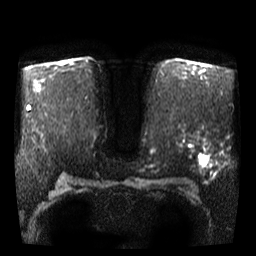
Breast MRI, one axial slice; slice 27 of 46 in the series (ordered by position); diffusion-weighted series; image 2 of 4 stored at this slice position (different b-values; order by instance number); 3 T; 256 × 256 image matrix, field of view 340 × 340 mm. Female patient.
Structures marked on this image (outlined manually by an expert reader):
- tumour on diffusion-weighted imaging: bounding box (x1, y1, x2, y2) in pixels: (200, 157, 207, 166)